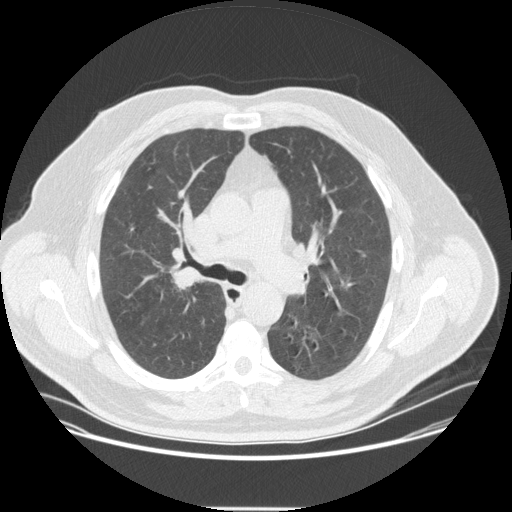
Low-dose screening chest CT, one axial slice; position 225 of 351 along the scan axis; lung window (W 1500 / L -600 HU); 2.5 mm slice thickness; 512 × 512 image matrix, field of view 419 × 419 mm.
Structures marked on this image (expert manual segmentation):
- lesion 1 (tumor, upper lobe of right lung): bounding box [x1, y1, x2, y2] px = [170, 270, 202, 290]